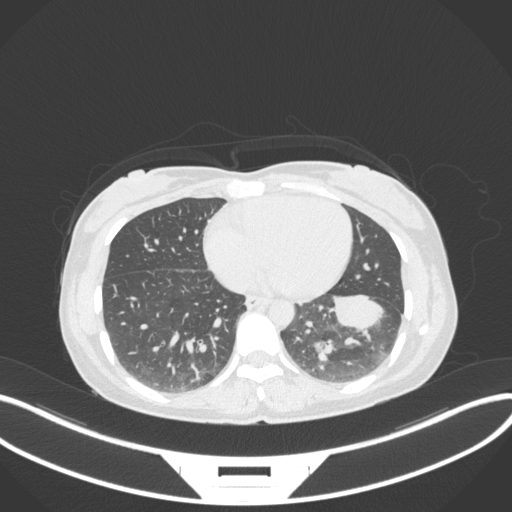
Chest CT, one axial slice; slice 132 of 361 in the series (ordered by position); reconstruction kernel B31f; lung window (W 1500 / L -600 HU); 1 mm slice thickness; 512 × 512 image matrix, field of view 400 × 400 mm. Female patient, age 41 years. Case-level facts recorded for this patient, not image findings: clinical TNM (as recorded): T2a N3 M1b.
Outlined on this slice (bounding box drawn by a radiologist):
- lung tumour (recorded histology: adenocarcinoma): bounding box [x1, y1, x2, y2] px = [330, 293, 388, 330]